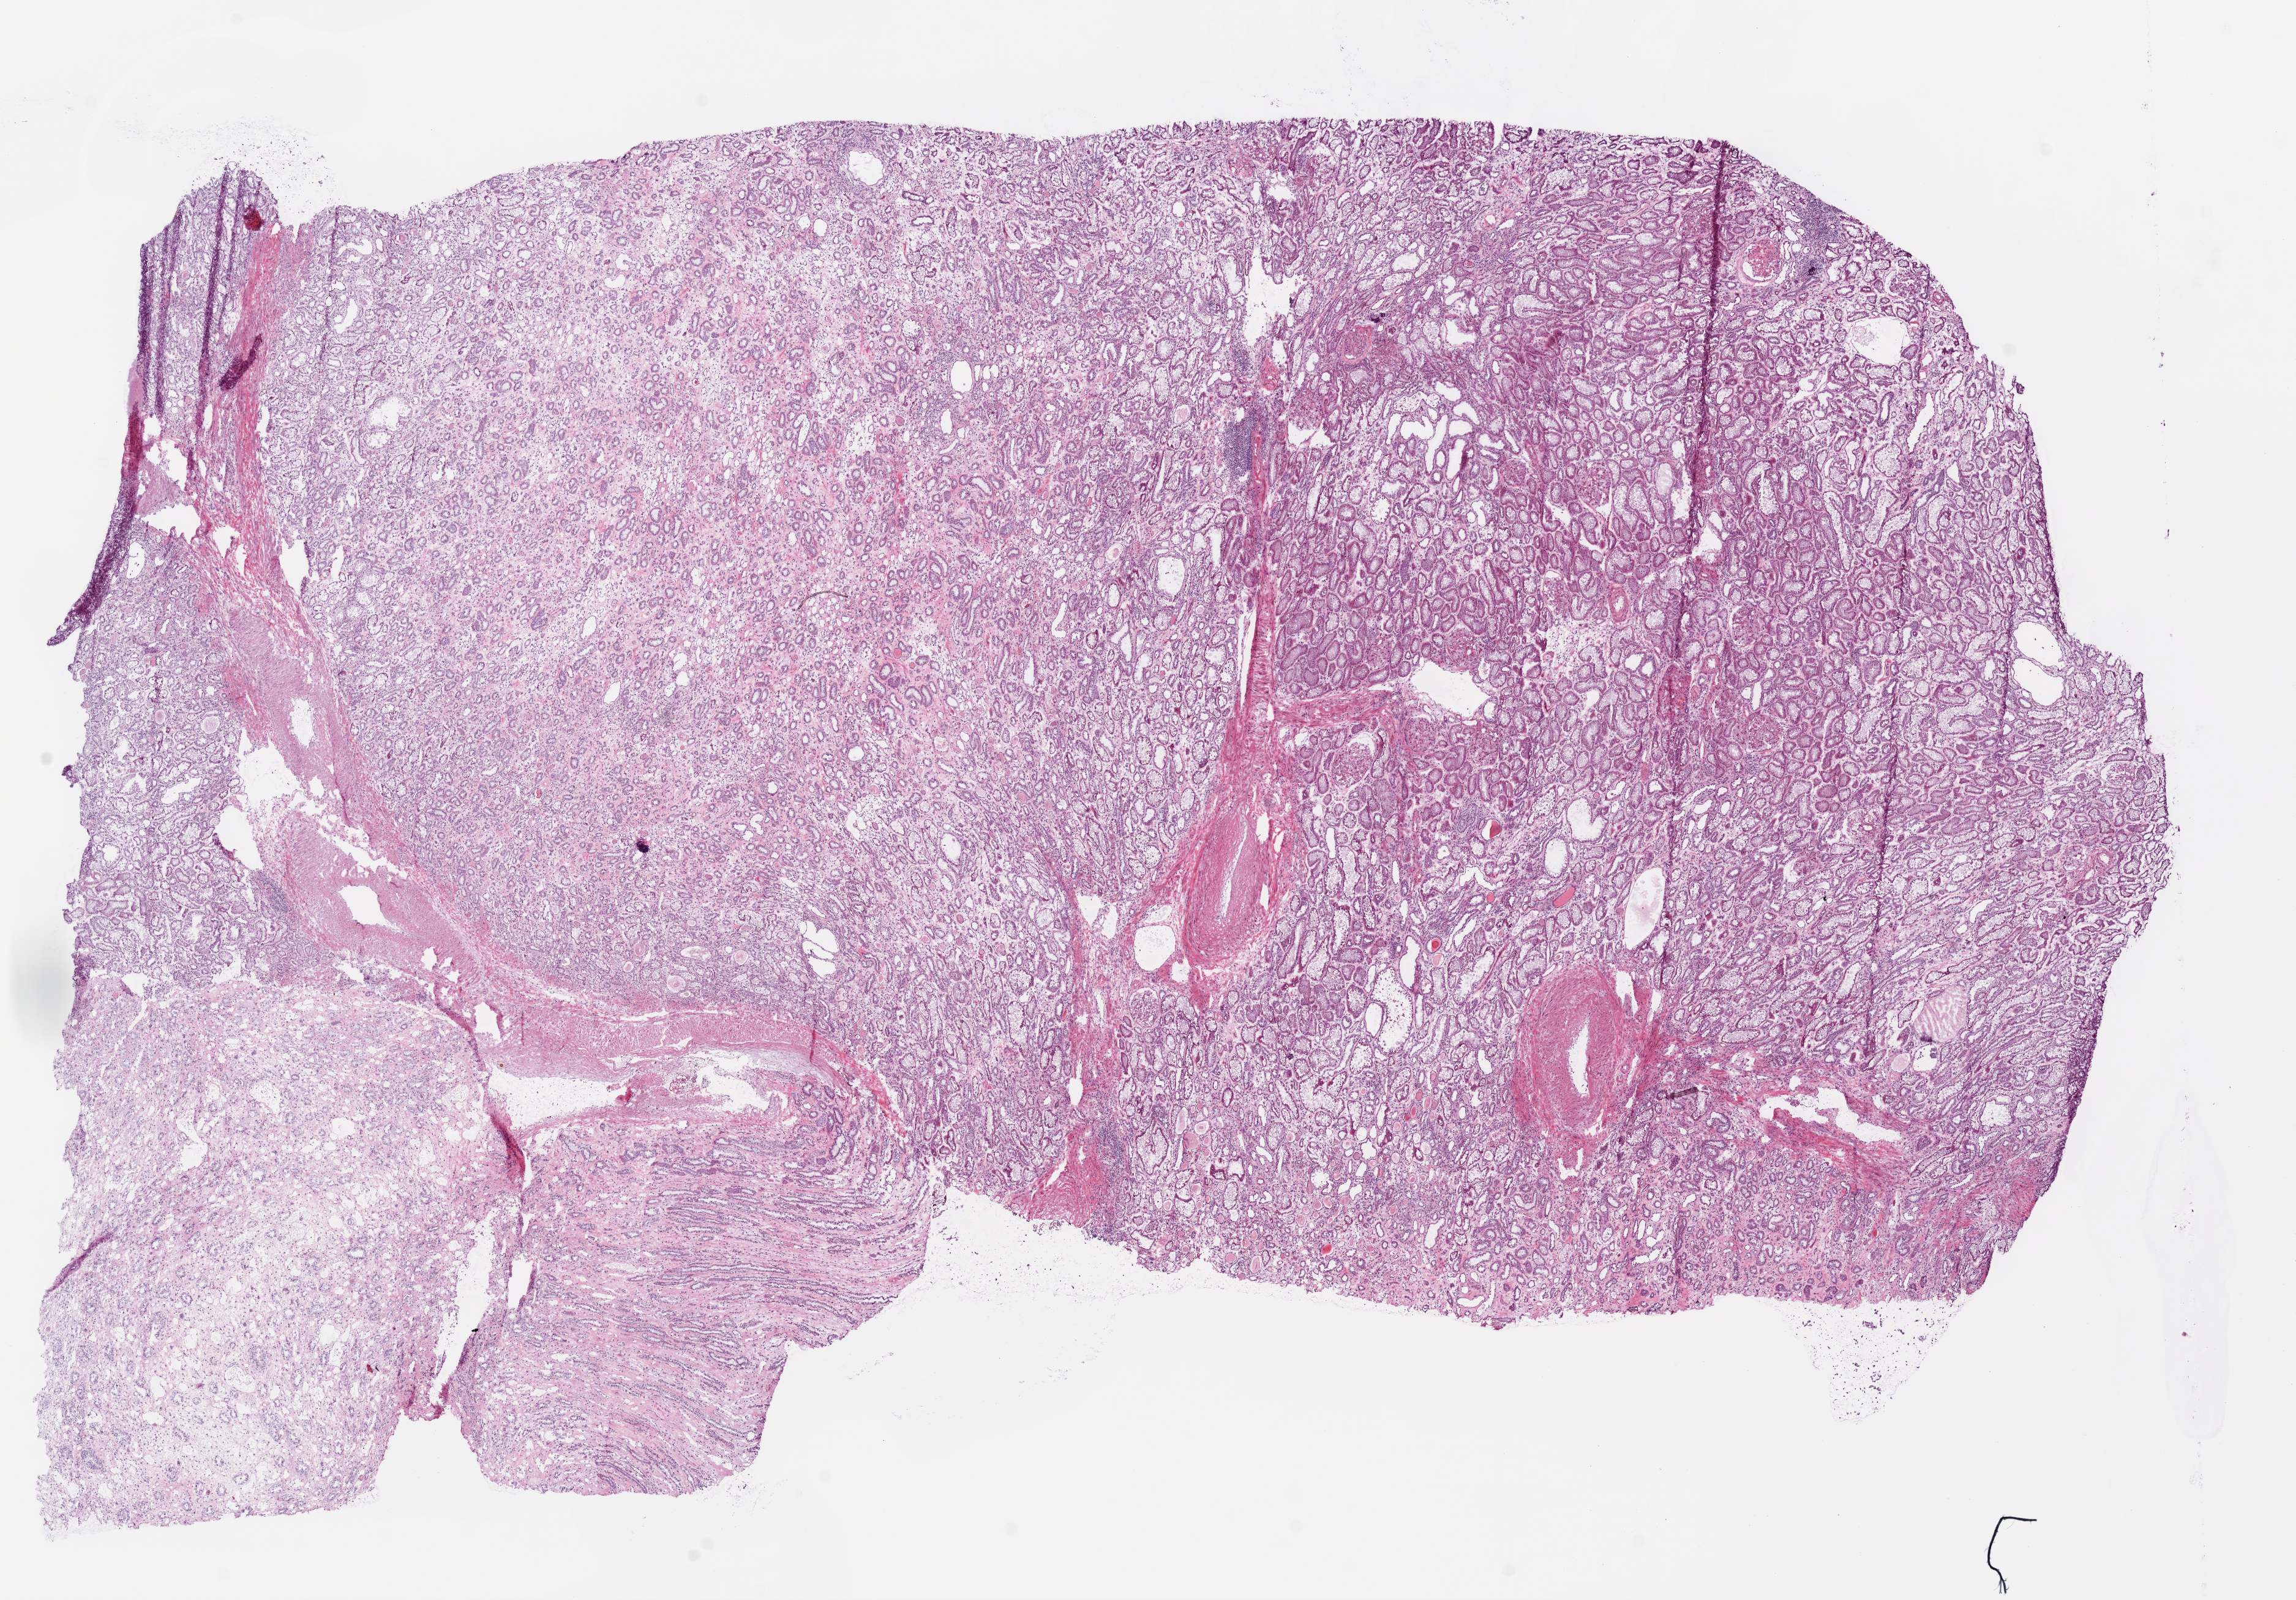
Whole-slide histology image, H&E-stained, a low-resolution overview of the entire scanned area, about 15.0 x 10.5 mm; frozen section from the bottom of the tissue portion; sample: solid tissue normal (non-tumour tissue), kidney. Female patient; age at initial diagnosis 72 years.
This section: solid tissue normal sample (biorepository sample class). Patient diagnosis: Clear cell adenocarcinoma, NOS.